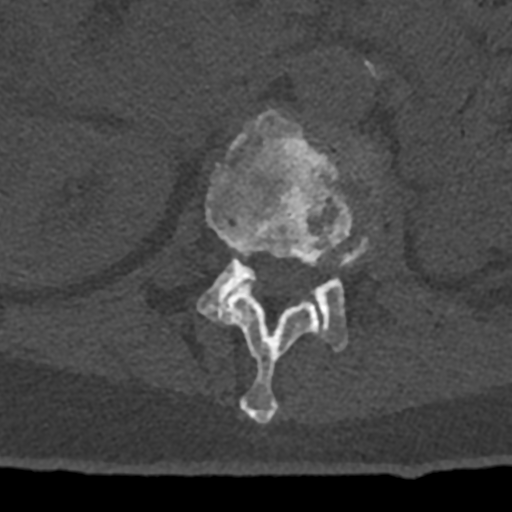
CT including the spine, one axial slice; position 410 of 797 along the scan axis; reconstruction kernel Br40s/3; 120 kVp; bone window (W 1800 / L 400 HU); 512 × 512 image matrix, field of view 160 × 160 mm. Patient: male, 74 years. Case-level facts recorded for this patient, not image findings: primary cancer: renal; vertebrae with lytic lesions (as recorded): T10, L1, L2, L3, L4, L5.
Outlined on this slice (semi-automatic segmentation, software-assisted and operator-edited):
- L1 vertebra: bounding box <205,109,354,424> (left, top, right, bottom; pixels)
- L2 vertebra: <198,153,374,352>